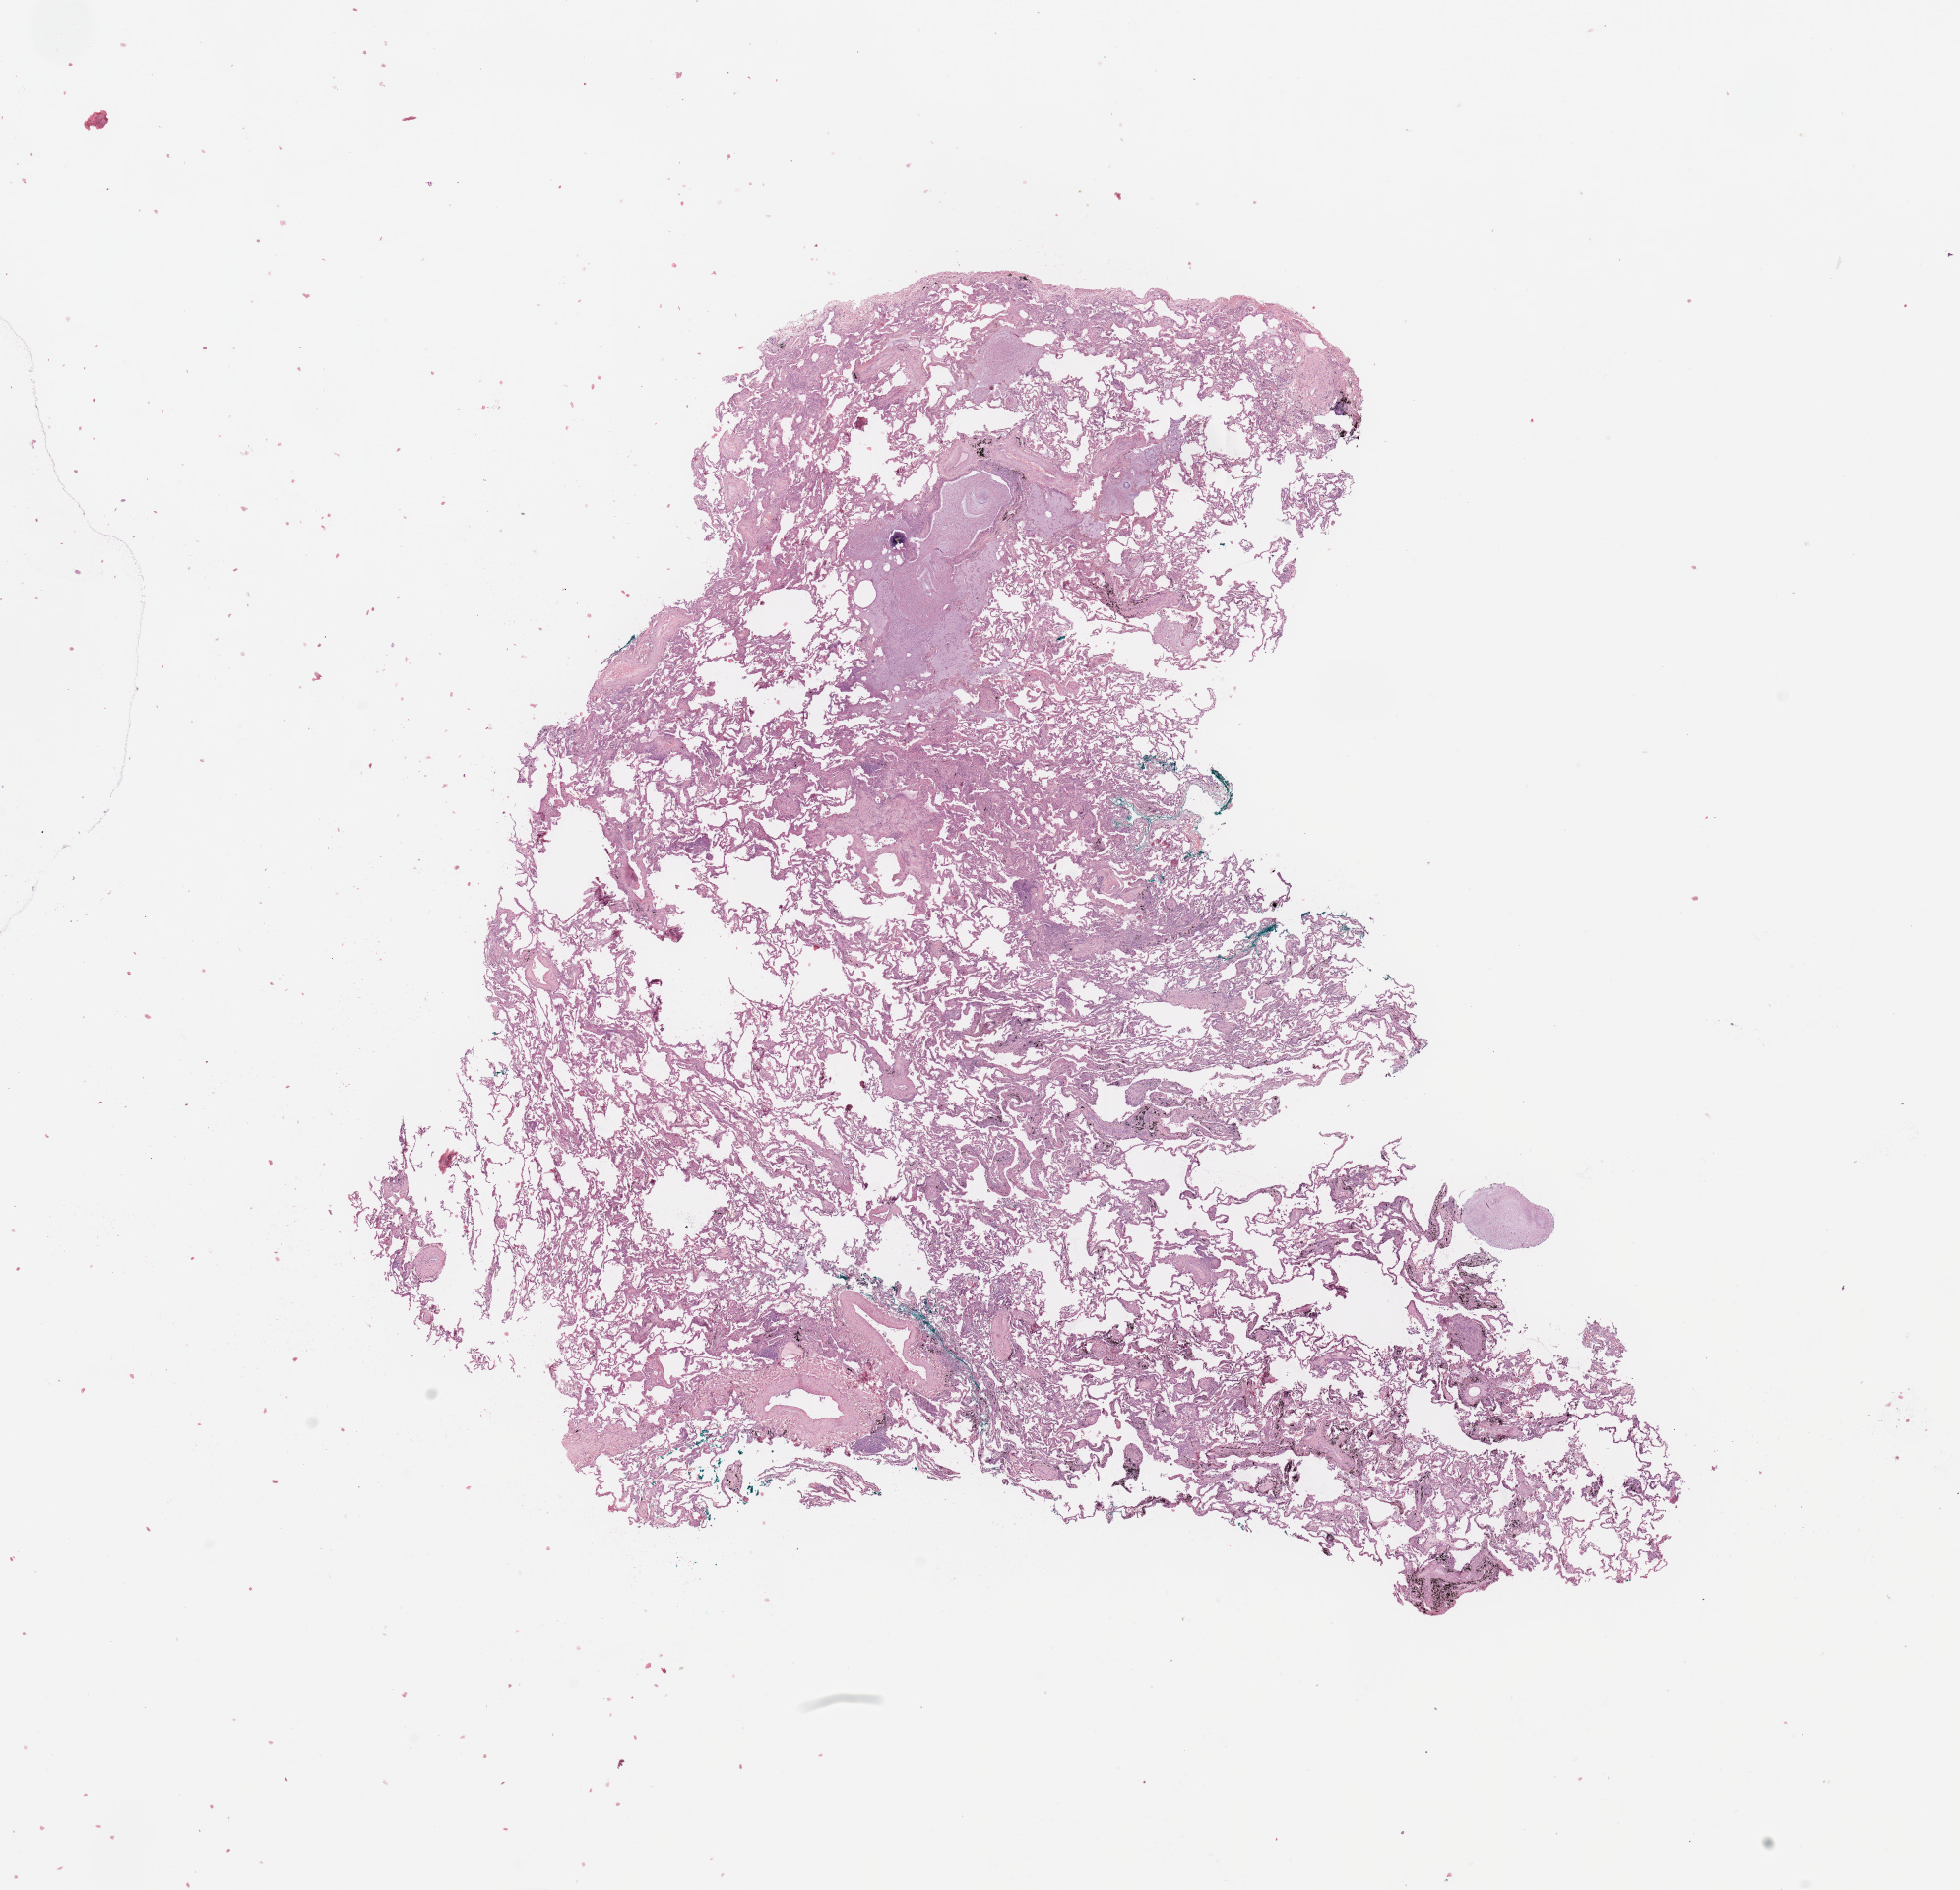
Digitized H&E tissue section (whole slide) — shown as a low-resolution overview of the whole scanned area (about 15.8 x 15.2 mm, from a 20x scan), normal (non-tumour) tissue sample, sampled site: lung. 75-year-old male patient.
This section: normal (non-tumour) tissue from the same patient. Patient diagnosis: Squamous cell carcinoma, NOS.